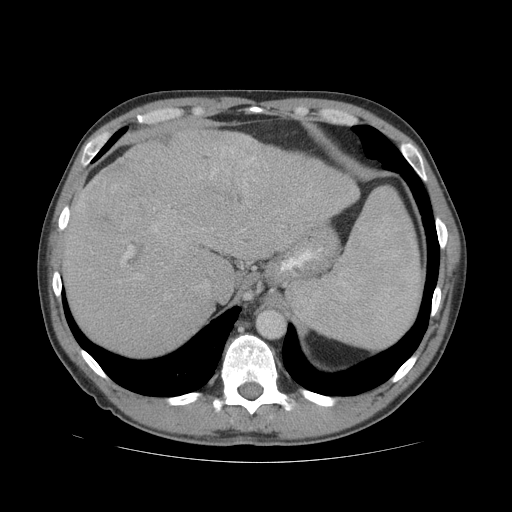
Contrast-enhanced abdominal CT (liver protocol), one axial slice; position 55 of 81 along the scan axis; reconstruction kernel STANDARD; soft-tissue window (W 400 / L 40 HU); 2.5 mm slice thickness; 512 × 512 image matrix. Case-level facts recorded for this patient, not image findings: diagnosis: hepatocellular carcinoma (patient treated with transarterial chemoembolisation; whether this scan precedes or follows treatment is not stated here); TNM stage (as recorded): Stage-IVB; Child-Pugh class: B; tumour nodularity: multinodular.
Annotated regions visible in this slice (semi-automatic segmentation, software-assisted and operator-edited):
- liver parenchyma outside the tumour (the mass and vessels are separate outlines, so this box may not span the whole liver): bounding box [x1, y1, x2, y2] px = [62, 128, 358, 356]
- mass: [82, 126, 251, 238]
- liver vessels: [80, 156, 256, 263]